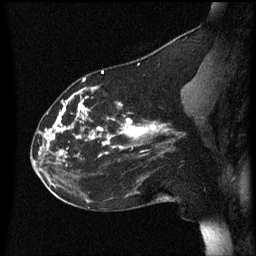
Breast MRI (dynamic contrast-enhanced), one sagittal slice. Dynamic contrast-enhanced series, image 2 of 3 at this slice position (ordered by acquisition). 1.5 T. TE 4.2 ms, TR 8.4 ms. 256 × 256 image matrix, field of view 200 × 200 mm. Patient: female, 35 years. From the clinical record (not read from this slice): setting: breast cancer imaged before/during neoadjuvant chemotherapy; receptor status: HER2-positive.
Structures marked on this image (semi-automatic segmentation, software-assisted and operator-edited):
- analysis volume of interest (the breast-tissue region the enhancement analysis was run in; not a lesion): bounding box (x1, y1, x2, y2) in pixels: (32, 72, 178, 173)
- tumour enhancement mask (voxels above the 70 % enhancement threshold inside the analysis volume of interest): (40, 72, 168, 157)